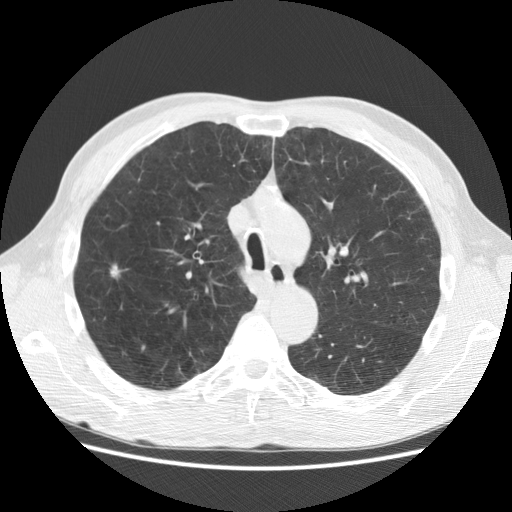
Low-dose screening chest CT, one axial slice. Position 206 of 282 along the scan axis. Reconstruction kernel STANDARD. 120 kVp. Lung window (W 1500 / L -600 HU). 2.5 mm slice thickness. 512 × 512 image matrix.
Annotated regions visible in this slice (outlined manually by an expert reader):
- lesion 1 (tumor, upper lobe of right lung): bounding box <111,265,119,277> (left, top, right, bottom; pixels)